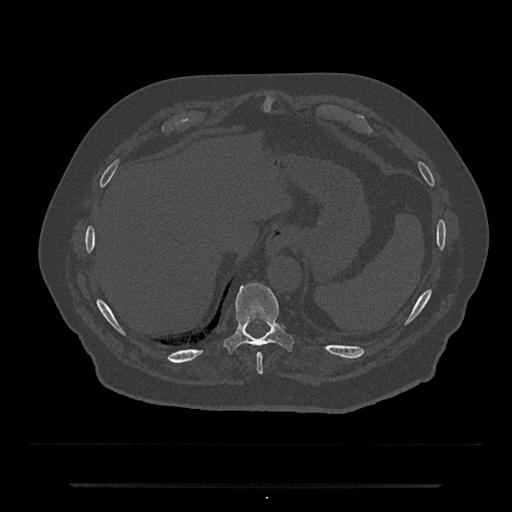
CT including the spine, one axial slice; position 712 of 797 along the scan axis; reconstruction kernel Br40s/3; bone window (W 1800 / L 400 HU); 512 × 512 image matrix, field of view 434 × 434 mm. Male patient, age 80 years. From the clinical record (not read from this slice): primary cancer: prostate; vertebrae with lytic lesions (as recorded): L1, T11.
Structures marked on this image (semi-automatic segmentation, software-assisted and operator-edited):
- T10 vertebra: box from (x=224, y=283) to (x=293, y=353) px
- T9 vertebra: (x=257, y=353)–(x=264, y=375)